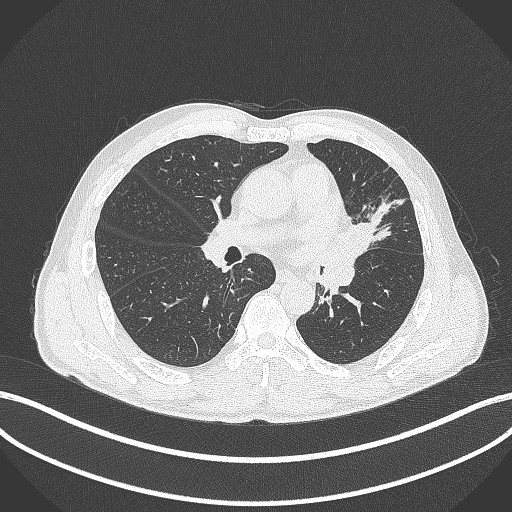
Chest CT, one axial slice. Position 228 of 429 along the scan axis. Reconstruction kernel B70f. Lung window (W 1500 / L -600 HU). 1 mm slice thickness. 512 × 512 image matrix, field of view 400 × 400 mm. Male patient, age 57 years. From the clinical record (not read from this slice): clinical TNM (as recorded): T2b N0 M0.
Outlined on this slice (bounding box drawn by a radiologist):
- lung tumour (recorded histology: squamous cell carcinoma): bounding box (x1, y1, x2, y2) in pixels: (339, 213, 377, 282)